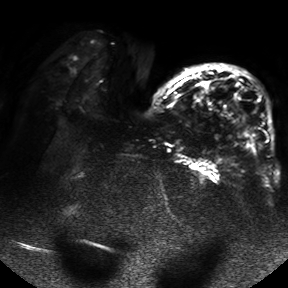
Breast MRI, one axial slice. Position 20 of 50 along the scan axis. Diffusion-weighted series; image 2 of 4 stored at this slice position (different b-values; order by instance number). 1.5 T. 4 mm slice thickness. 288 × 288 image matrix, field of view 390 × 390 mm. Female patient.
Outlined on this slice (outlined manually by an expert reader):
- tumour on diffusion-weighted imaging: bounding box <233,102,248,135> (left, top, right, bottom; pixels)